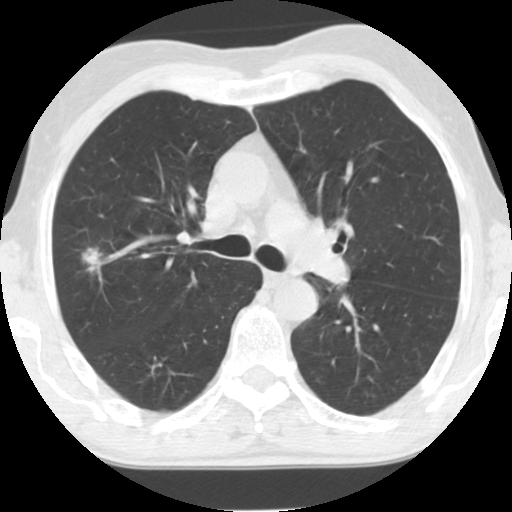
Axial slice from a low-dose chest CT screening exam. Second screening round (one year after baseline). Lung window (W 1500 / L -600 HU). Standard (soft-tissue) reconstruction kernel (STANDARD). Slice 43 of 124 in the series. Male, age 69 years at enrolment. Former smoker at enrolment.
• Expert reader's lesion annotation, bounding box <67,232,122,290> (left, top, right, bottom; pixels).
• Screening reader's record for this exam (one nodule recorded; not confirmed to be the boxed lesion): non-calcified nodule or mass ≥4 mm, right upper lobe, 12 × 8 mm, spiculated (stellate) margins, soft tissue attenuation, pre-existing on the prior screen: yes; interval growth: yes.
• Official screen result: positive, other.